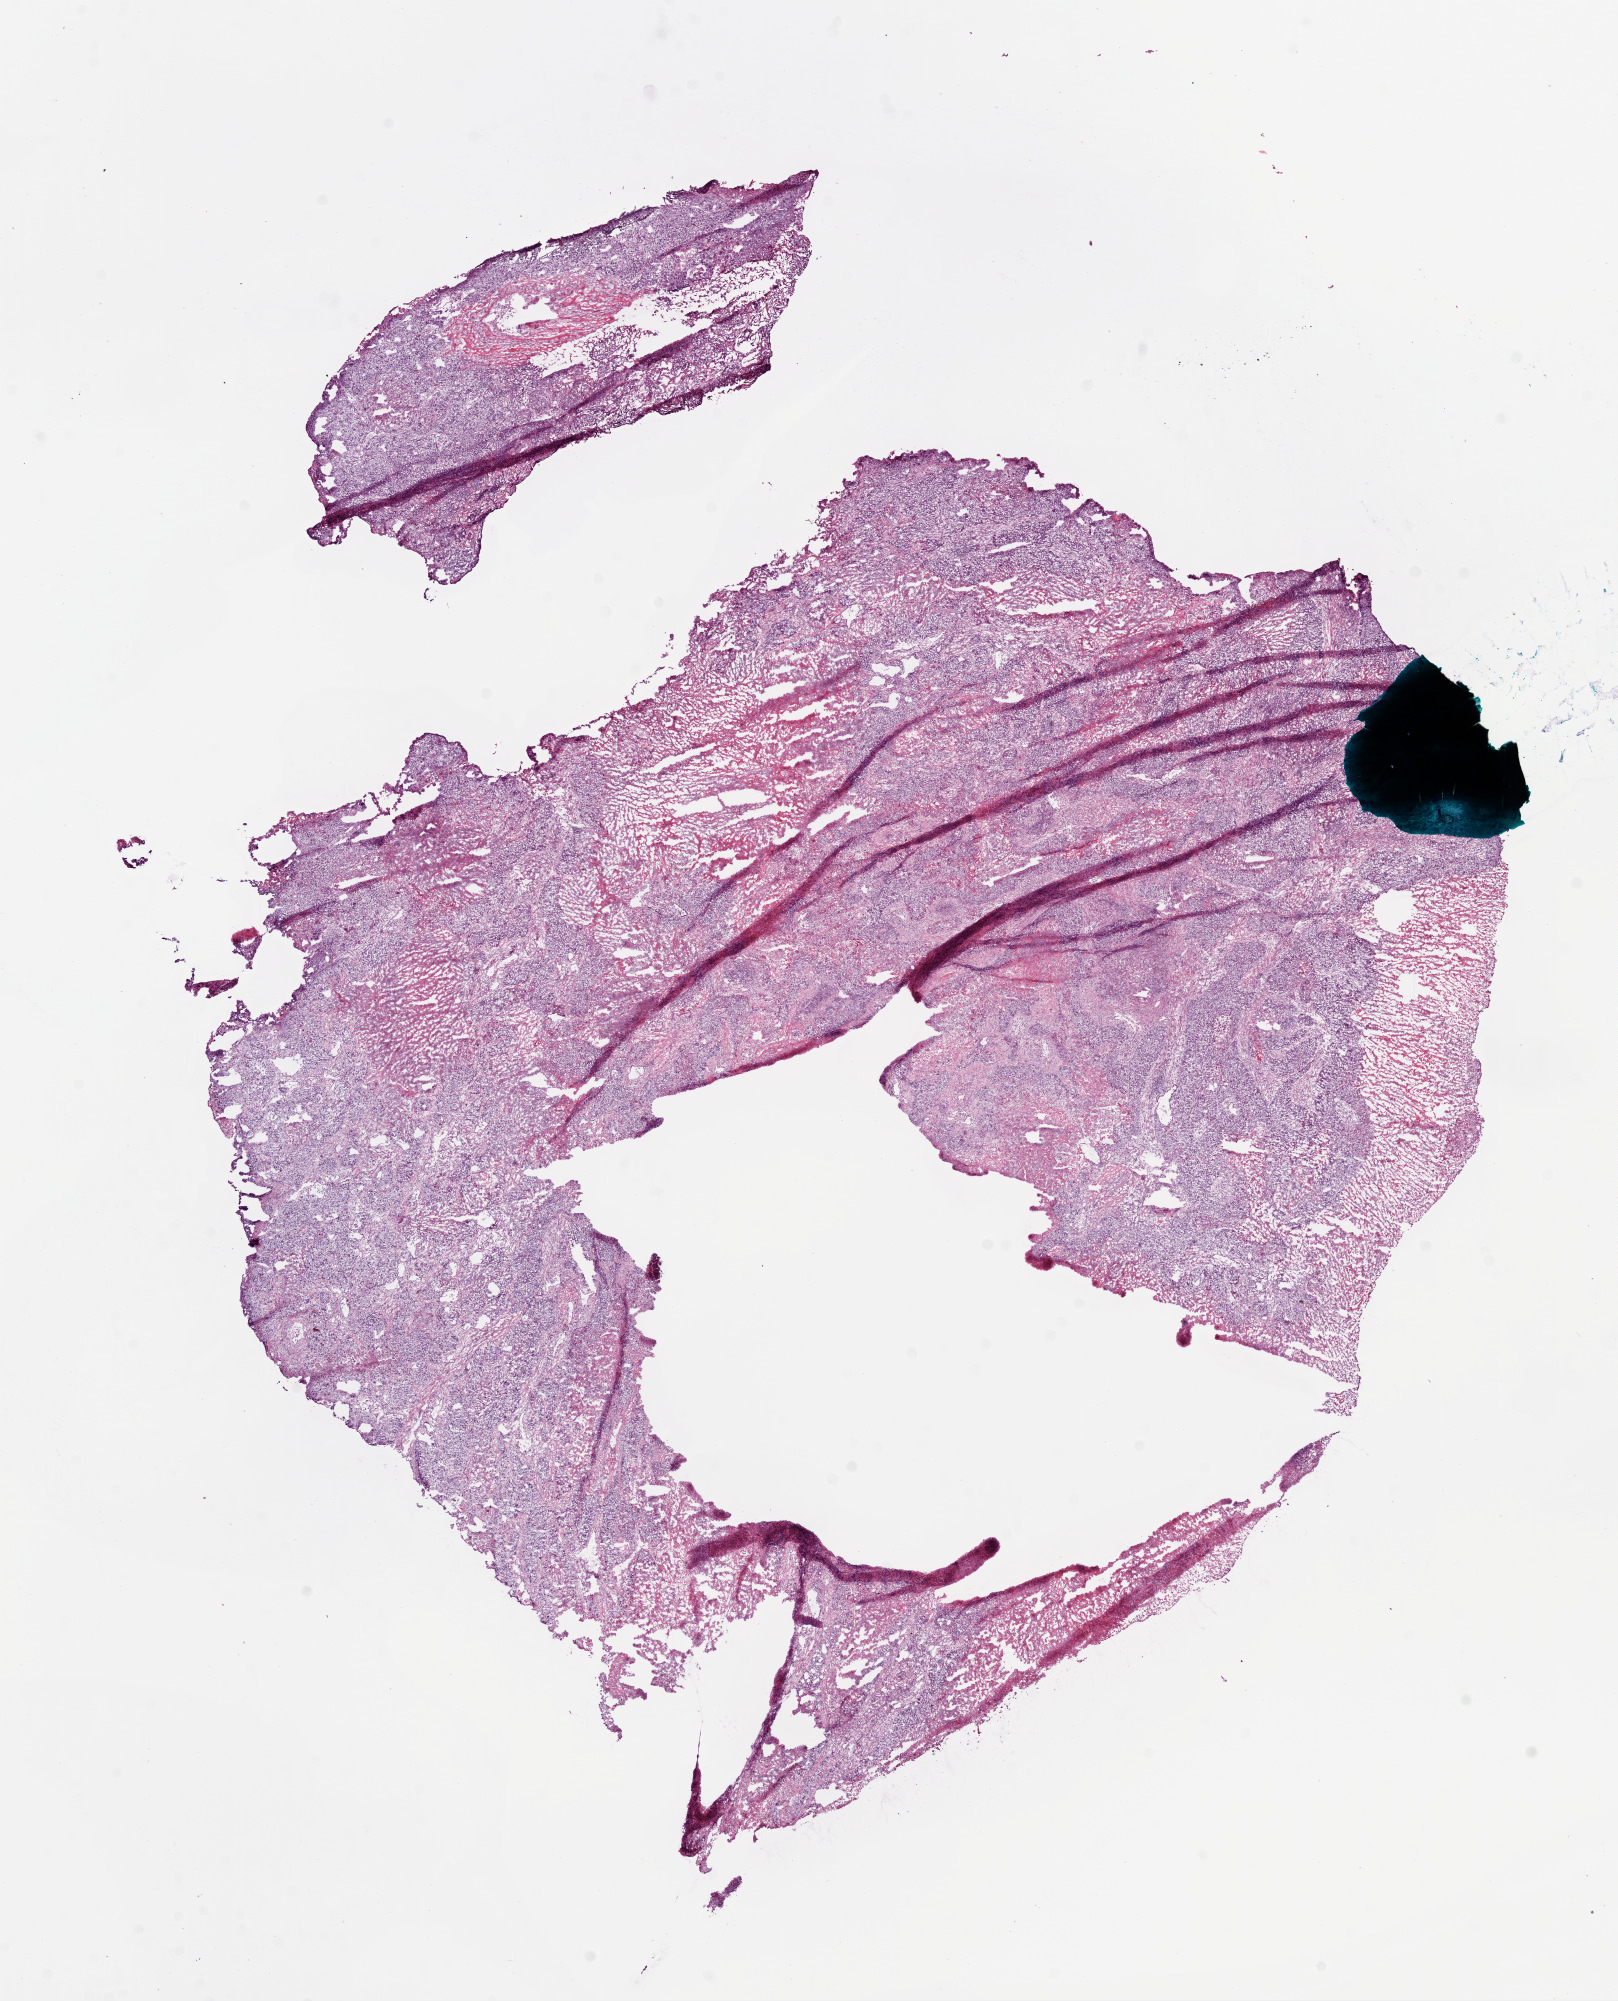
H&E whole-slide image, whole scanned area (about 13.1 x 16.1 mm, slide scanned at 20x) shown as a low-resolution overview, frozen section from the bottom of the tissue portion, primary tumour sample from the lung. Male, age 67 years at initial diagnosis. Composition of this section per pathologist review: tumour nuclei 90%, necrosis 15%.
- laterality: right
- AJCC pathologic stage: IB
- TNM: T2 N0 M0
- pathologic diagnosis: Squamous cell carcinoma, NOS (upper lobe, lung)